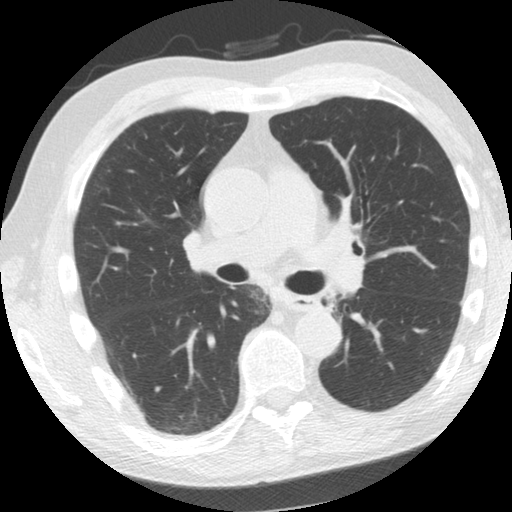
Low-dose screening chest CT, axial slice. Second annual screen. Lung window (W 1500 / L -600 HU). 2.5 mm slice thickness. Male participant, aged 61 years at enrolment. Former smoker at enrolment.
Expert reader's lesion annotation, bounding box (x1, y1, x2, y2) in pixels: (306, 286, 349, 321). Screening reader's record for this exam: no non-calcified nodule ≥4 mm recorded. Lung cancer was diagnosed 775 days after this screen: squamous cell carcinoma, NOS, left upper lobe, left lower lobe, well differentiated (G1), stage IIB (AJCC 6th edition), 100 mm at pathology.